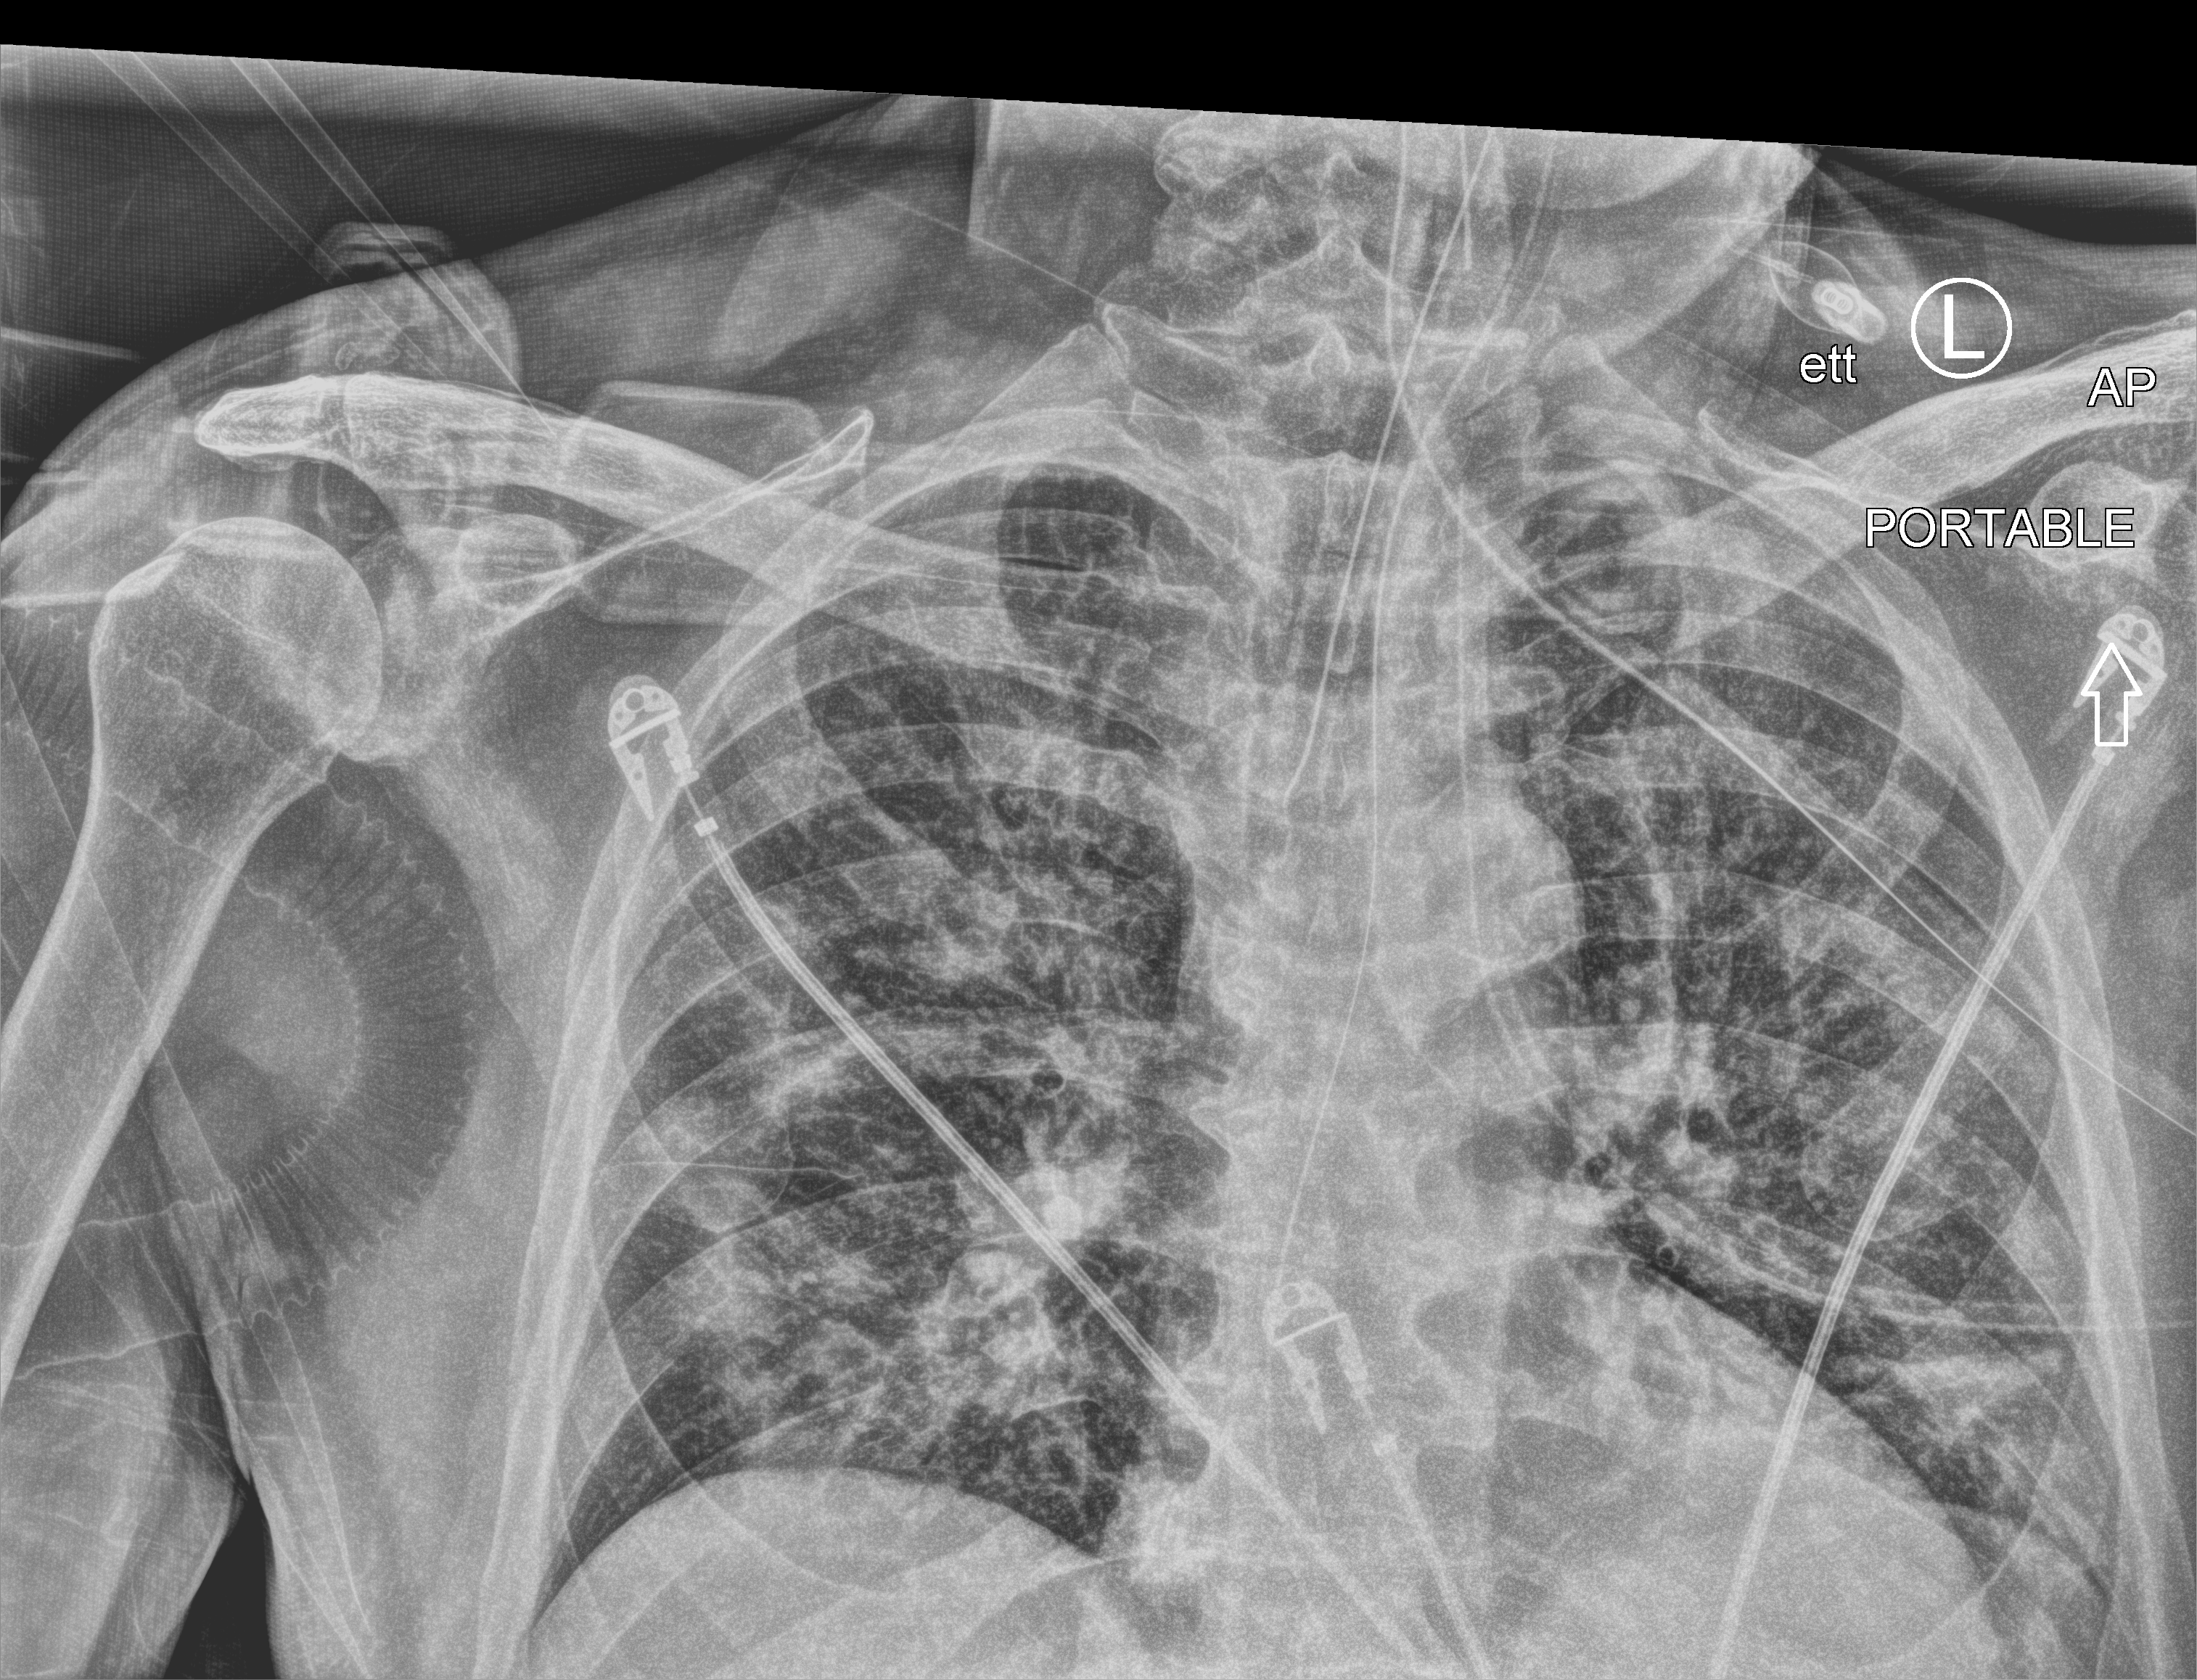
Chest X-ray (portable), anteroposterior (AP) projection. Patient hospitalised with COVID-19; male, aged 60–74 years.
Hospital-stay facts (about this admission, not read from this image; timing relative to this image not recorded): admitted to intensive care during this hospital stay: yes.